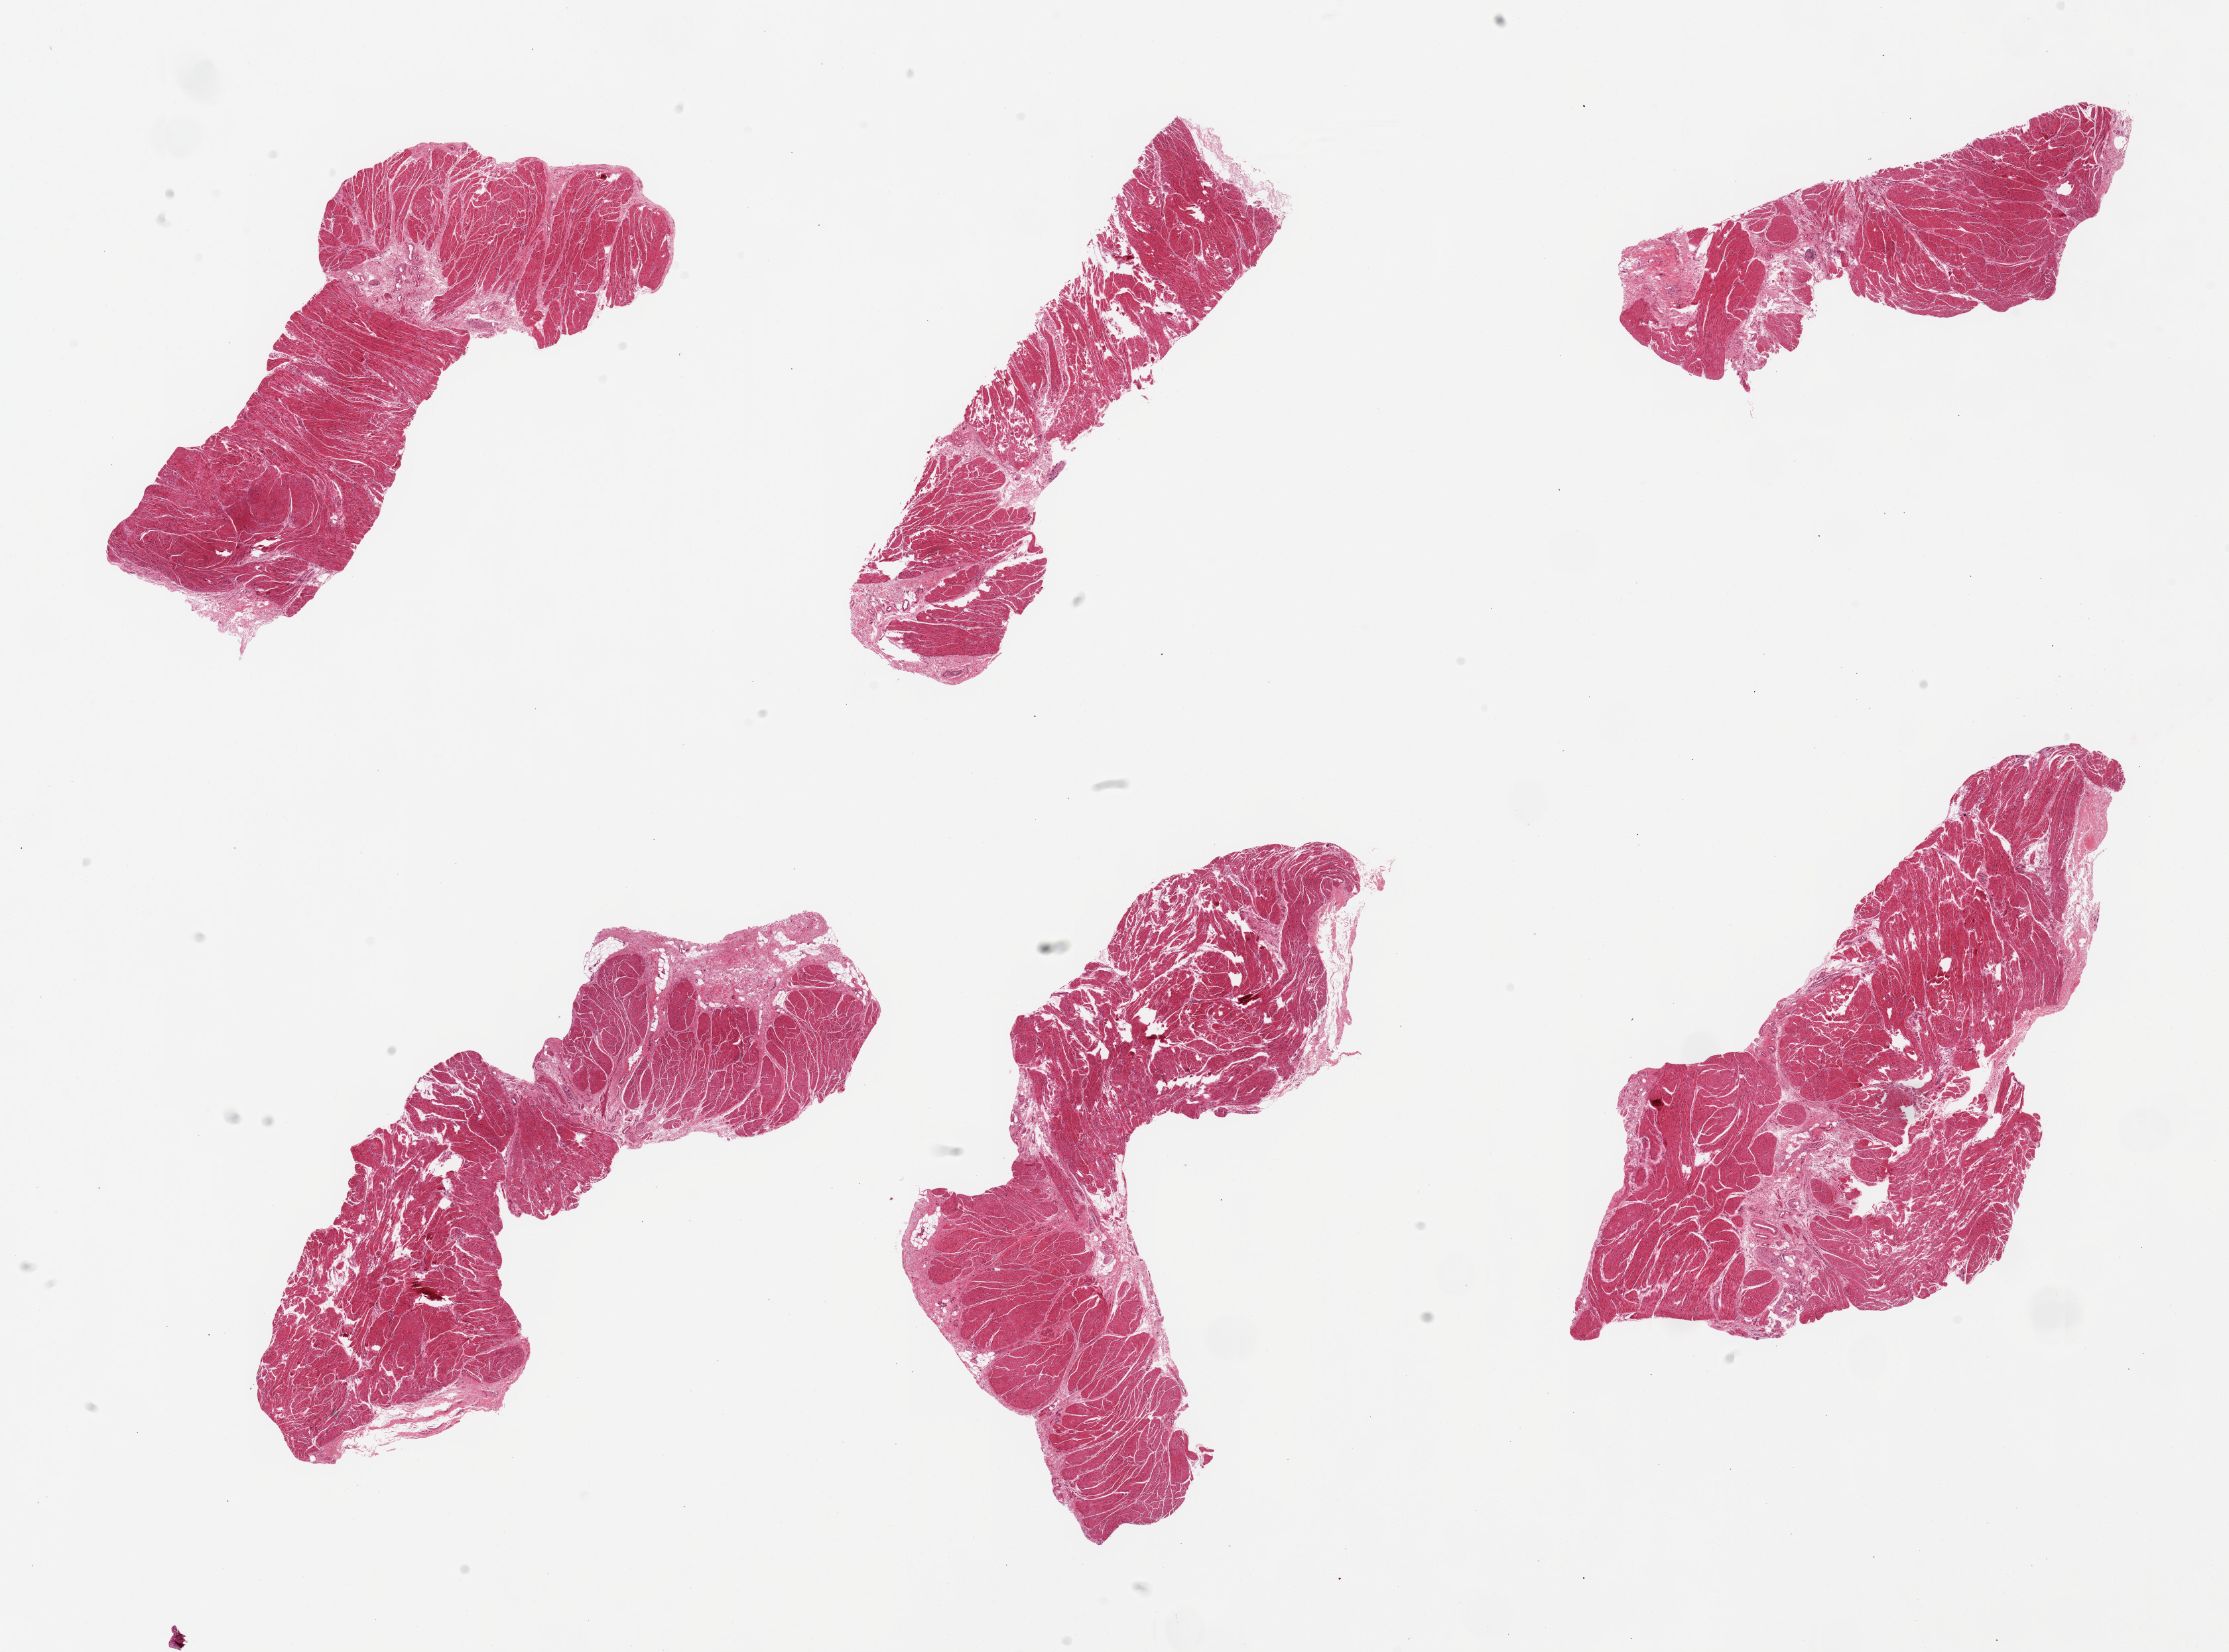
Whole-slide image, haematoxylin and eosin stain — low-resolution overview of the scanned area, about 26.6 x 19.7 mm, PAXgene-fixed, paraffin-embedded tissue, target tissue: gastroesophageal junction, tissue donor sample. Donor: female.
Review note (as recorded): 6 pieces, all muscularis, good specimens.